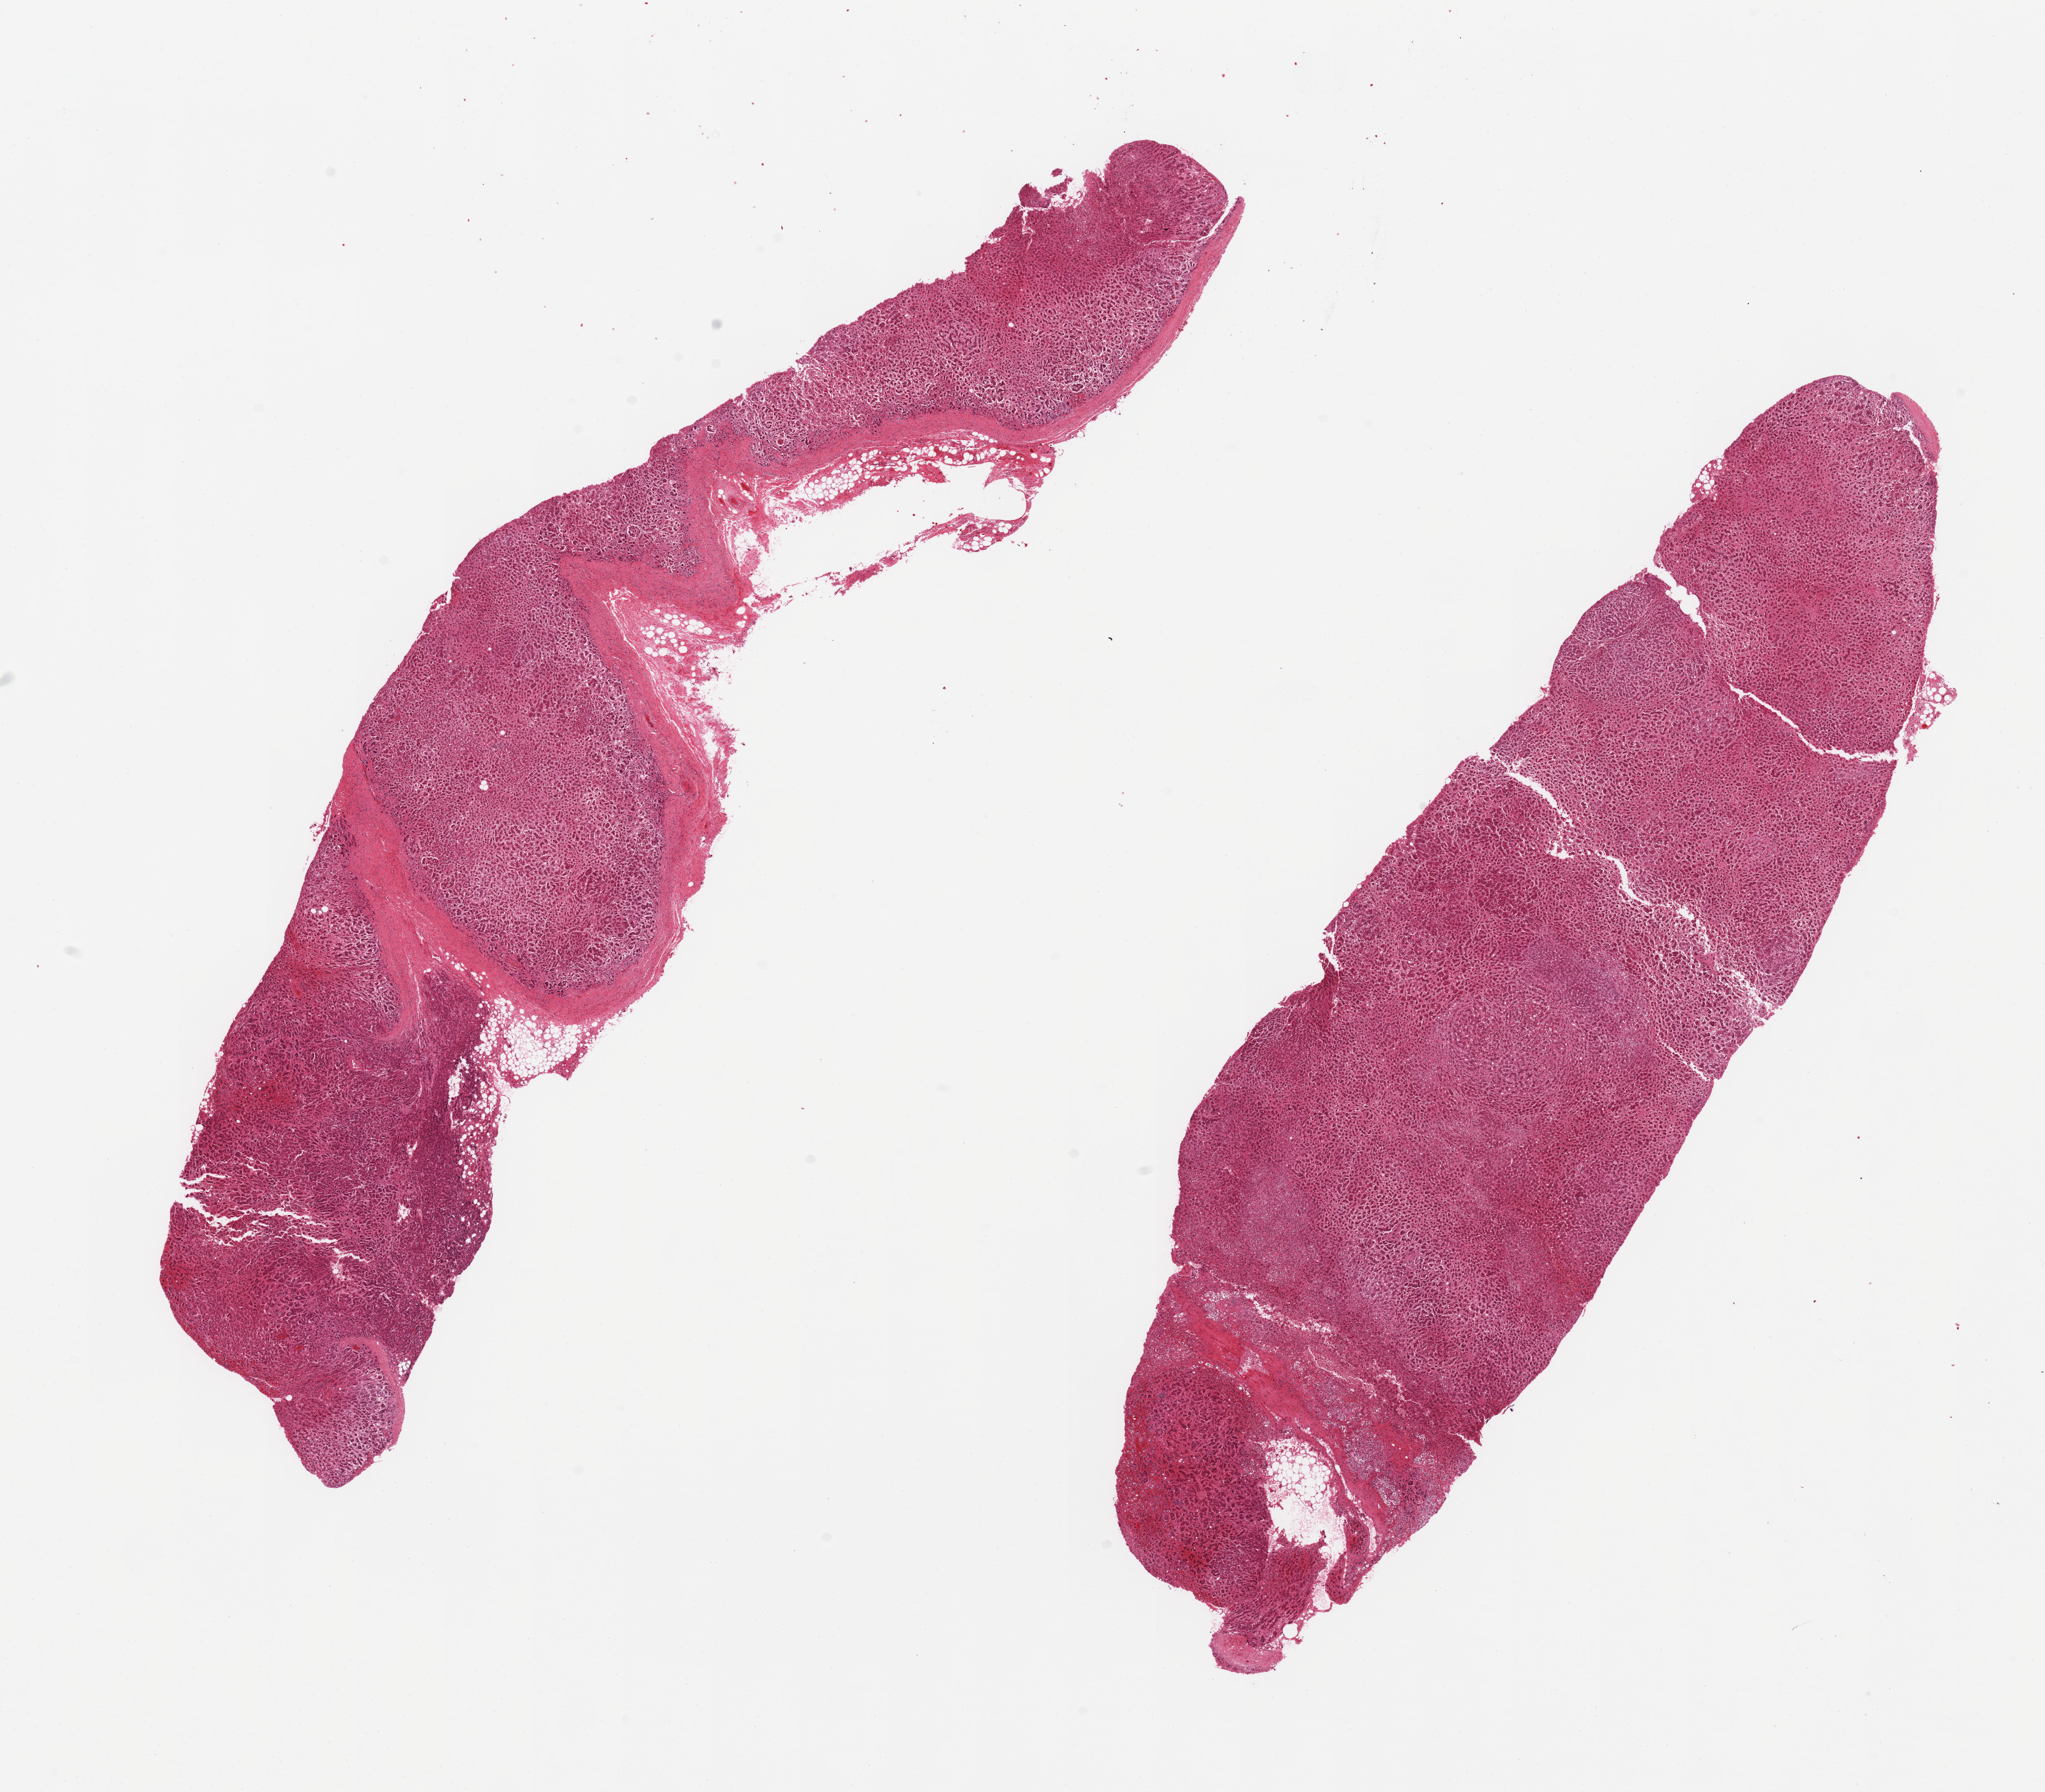
Digitized H&E-stained section, a low-resolution overview of the entire scanned area, about 22.6 x 19.8 mm (slide scanned at 20x); PAXgene-fixed paraffin-embedded (PFPE) section; sampled site (target tissue): adrenal gland; donor tissue sample.
Review note (as recorded): 2 pieces, all cortex, moderately autolyzed.